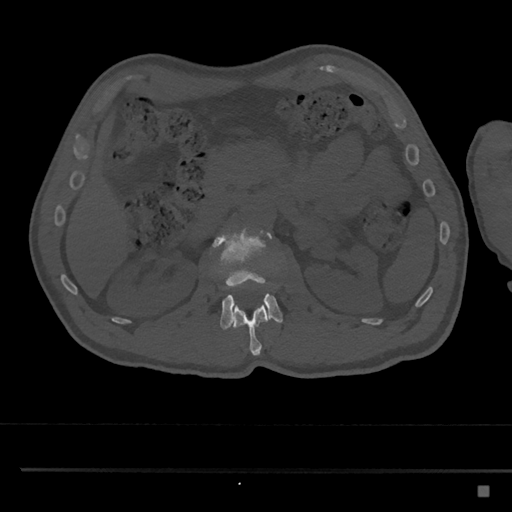
CT including the spine, one axial slice; slice 793 of 797 in the series (ordered by position); 120 kVp; bone window (W 1800 / L 400 HU); 0.5 mm slice thickness; 512 × 512 image matrix. Patient: male, 59 years. From the clinical record (not read from this slice): primary cancer: prostate.
Outlined on this slice (semi-automatic segmentation, software-assisted and operator-edited):
- L1 vertebra: bounding box (x1, y1, x2, y2) in pixels: (233, 301, 269, 356)
- L2 vertebra: (209, 227, 283, 330)